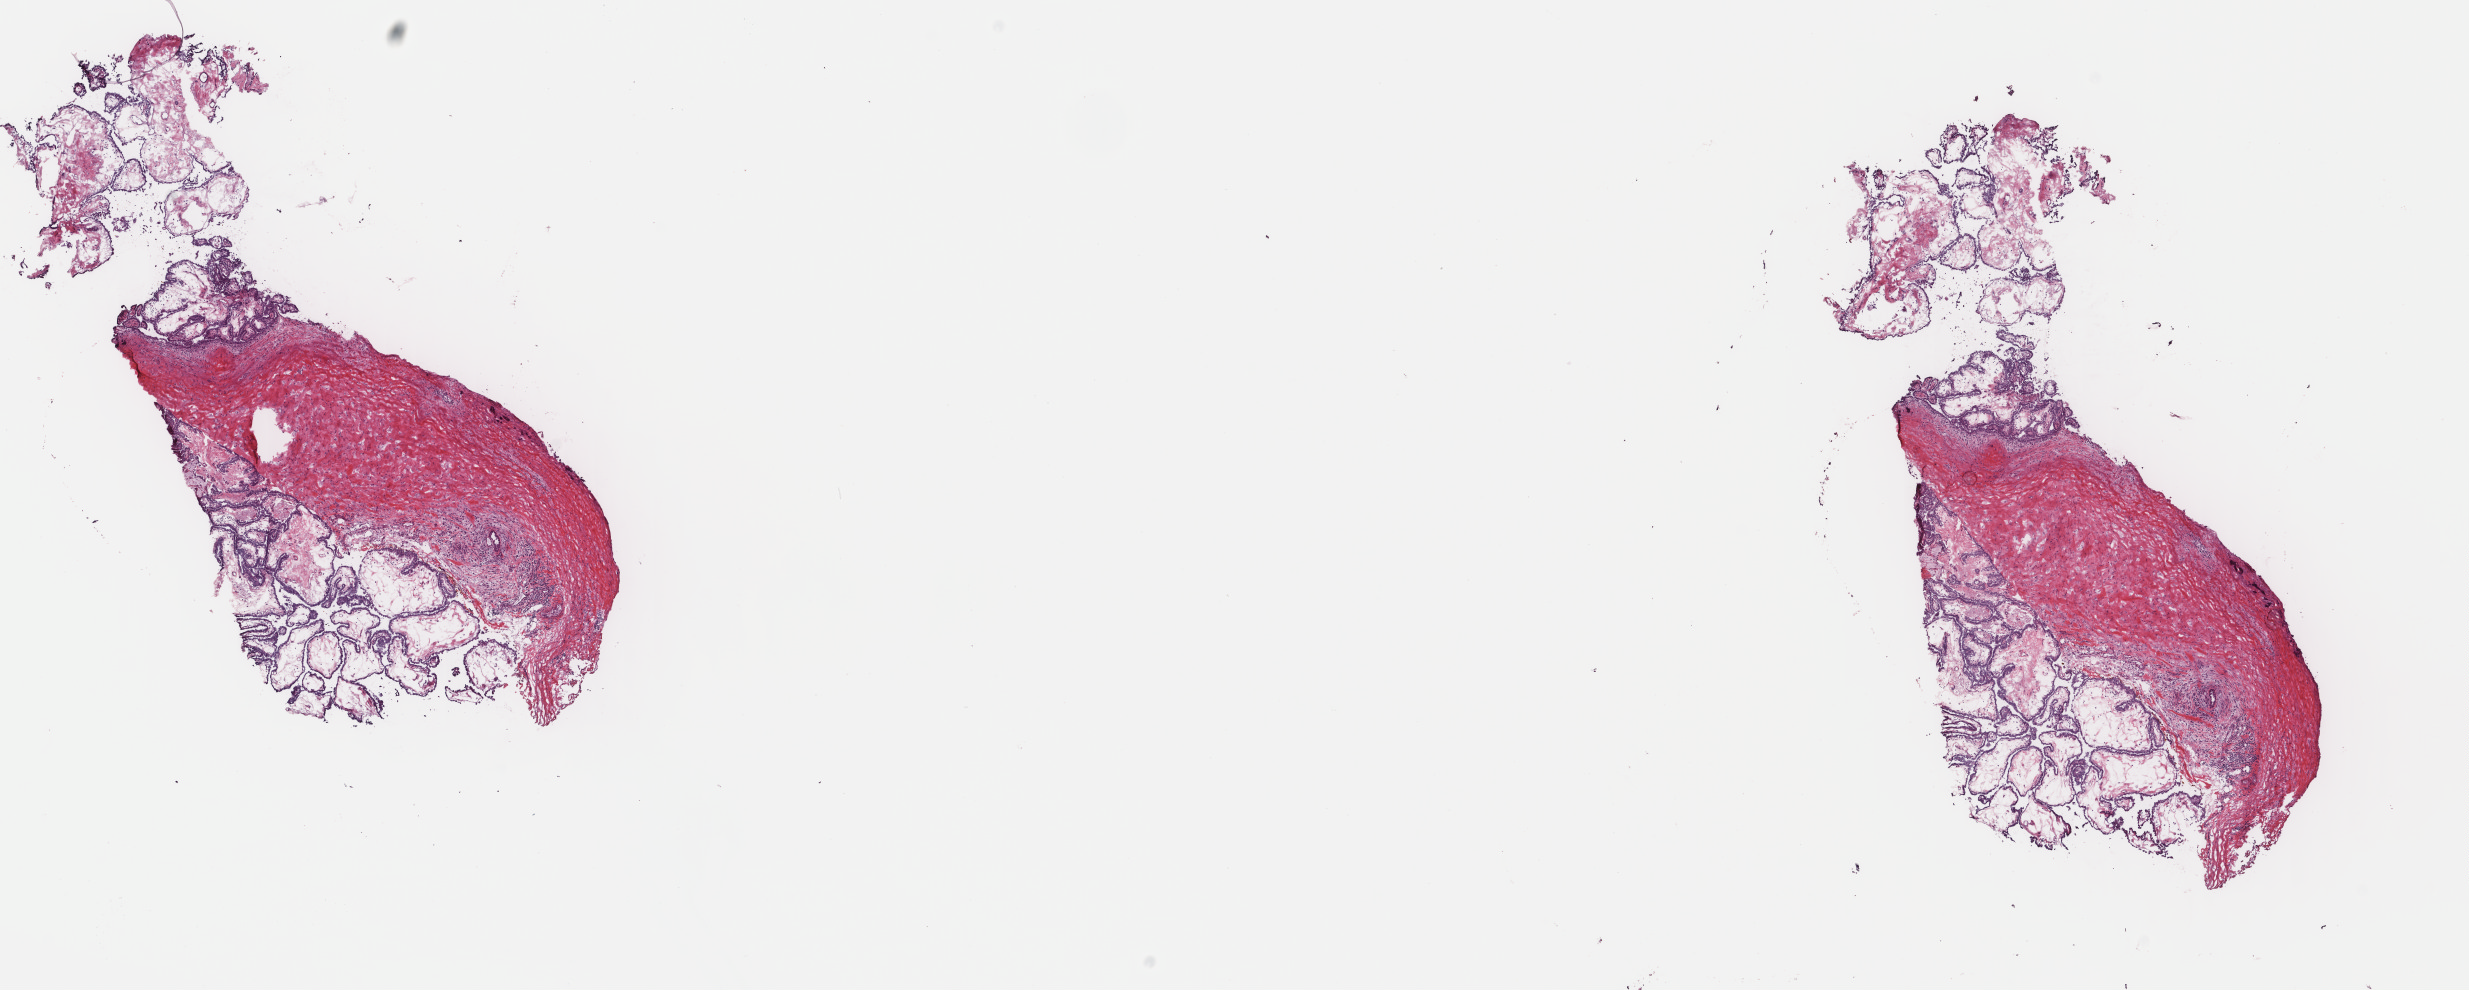
Digitized H&E-stained tissue section (whole slide), shown as a low-resolution overview of the whole scanned area (about 19.6 x 7.9 mm, slide scanned at 40x), frozen section from the top of the tissue portion, sample: primary tumour, thyroid. Male patient; age at initial diagnosis 28 years. Composition of this section per pathologist review: tumour cells 70%, tumour nuclei 70%, normal cells 0%, stromal cells 30%, necrosis 0%. Infiltration values recorded for this section: lymphocyte infiltration 4%, monocyte infiltration 2%, neutrophil infiltration 1%.
Diagnosis: Papillary adenocarcinoma, NOS (thyroid gland). Laterality: left. AJCC pathologic stage: I (6th edition).